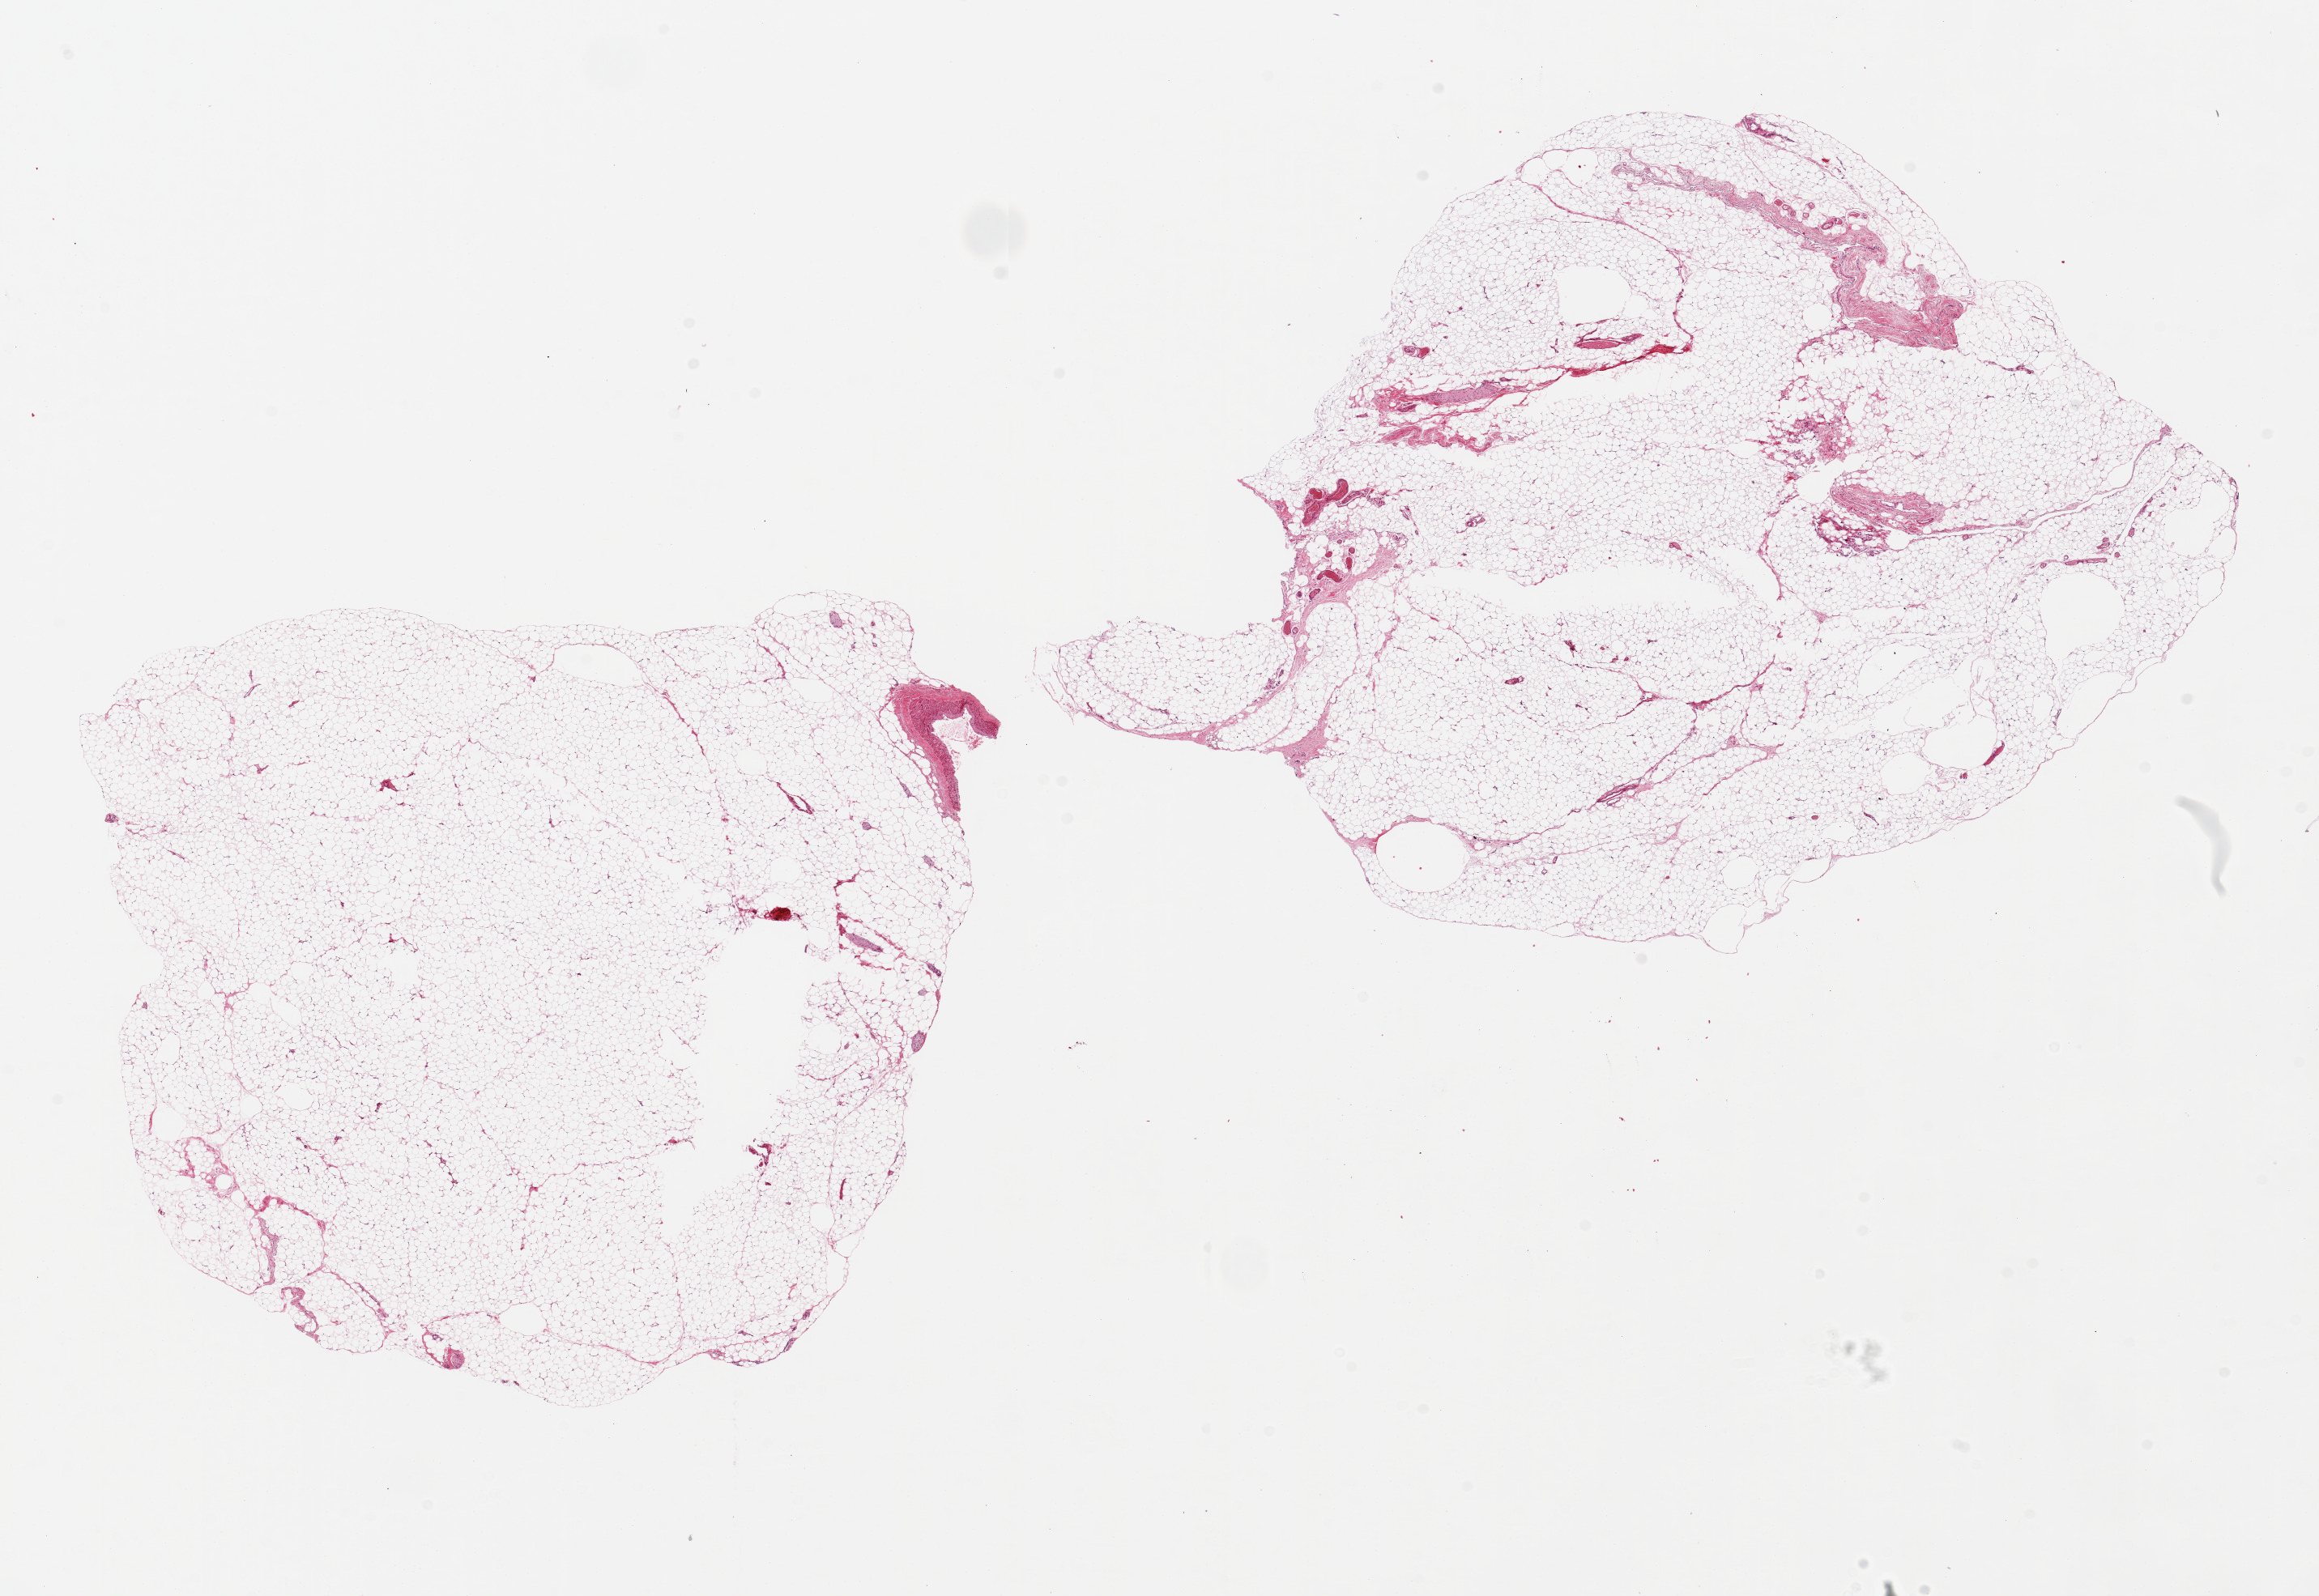
Digitized H&E-stained section, brightfield — whole scanned area (about 22.6 x 15.6 mm) shown as a low-resolution overview; PAXgene-fixed, paraffin-embedded tissue; sampled site (target tissue): omentum; tissue donor sample. Donor: female.
* pathologist's review note for this sample: 2 pieces, 9x8 & 9x8mm; central fragmentation